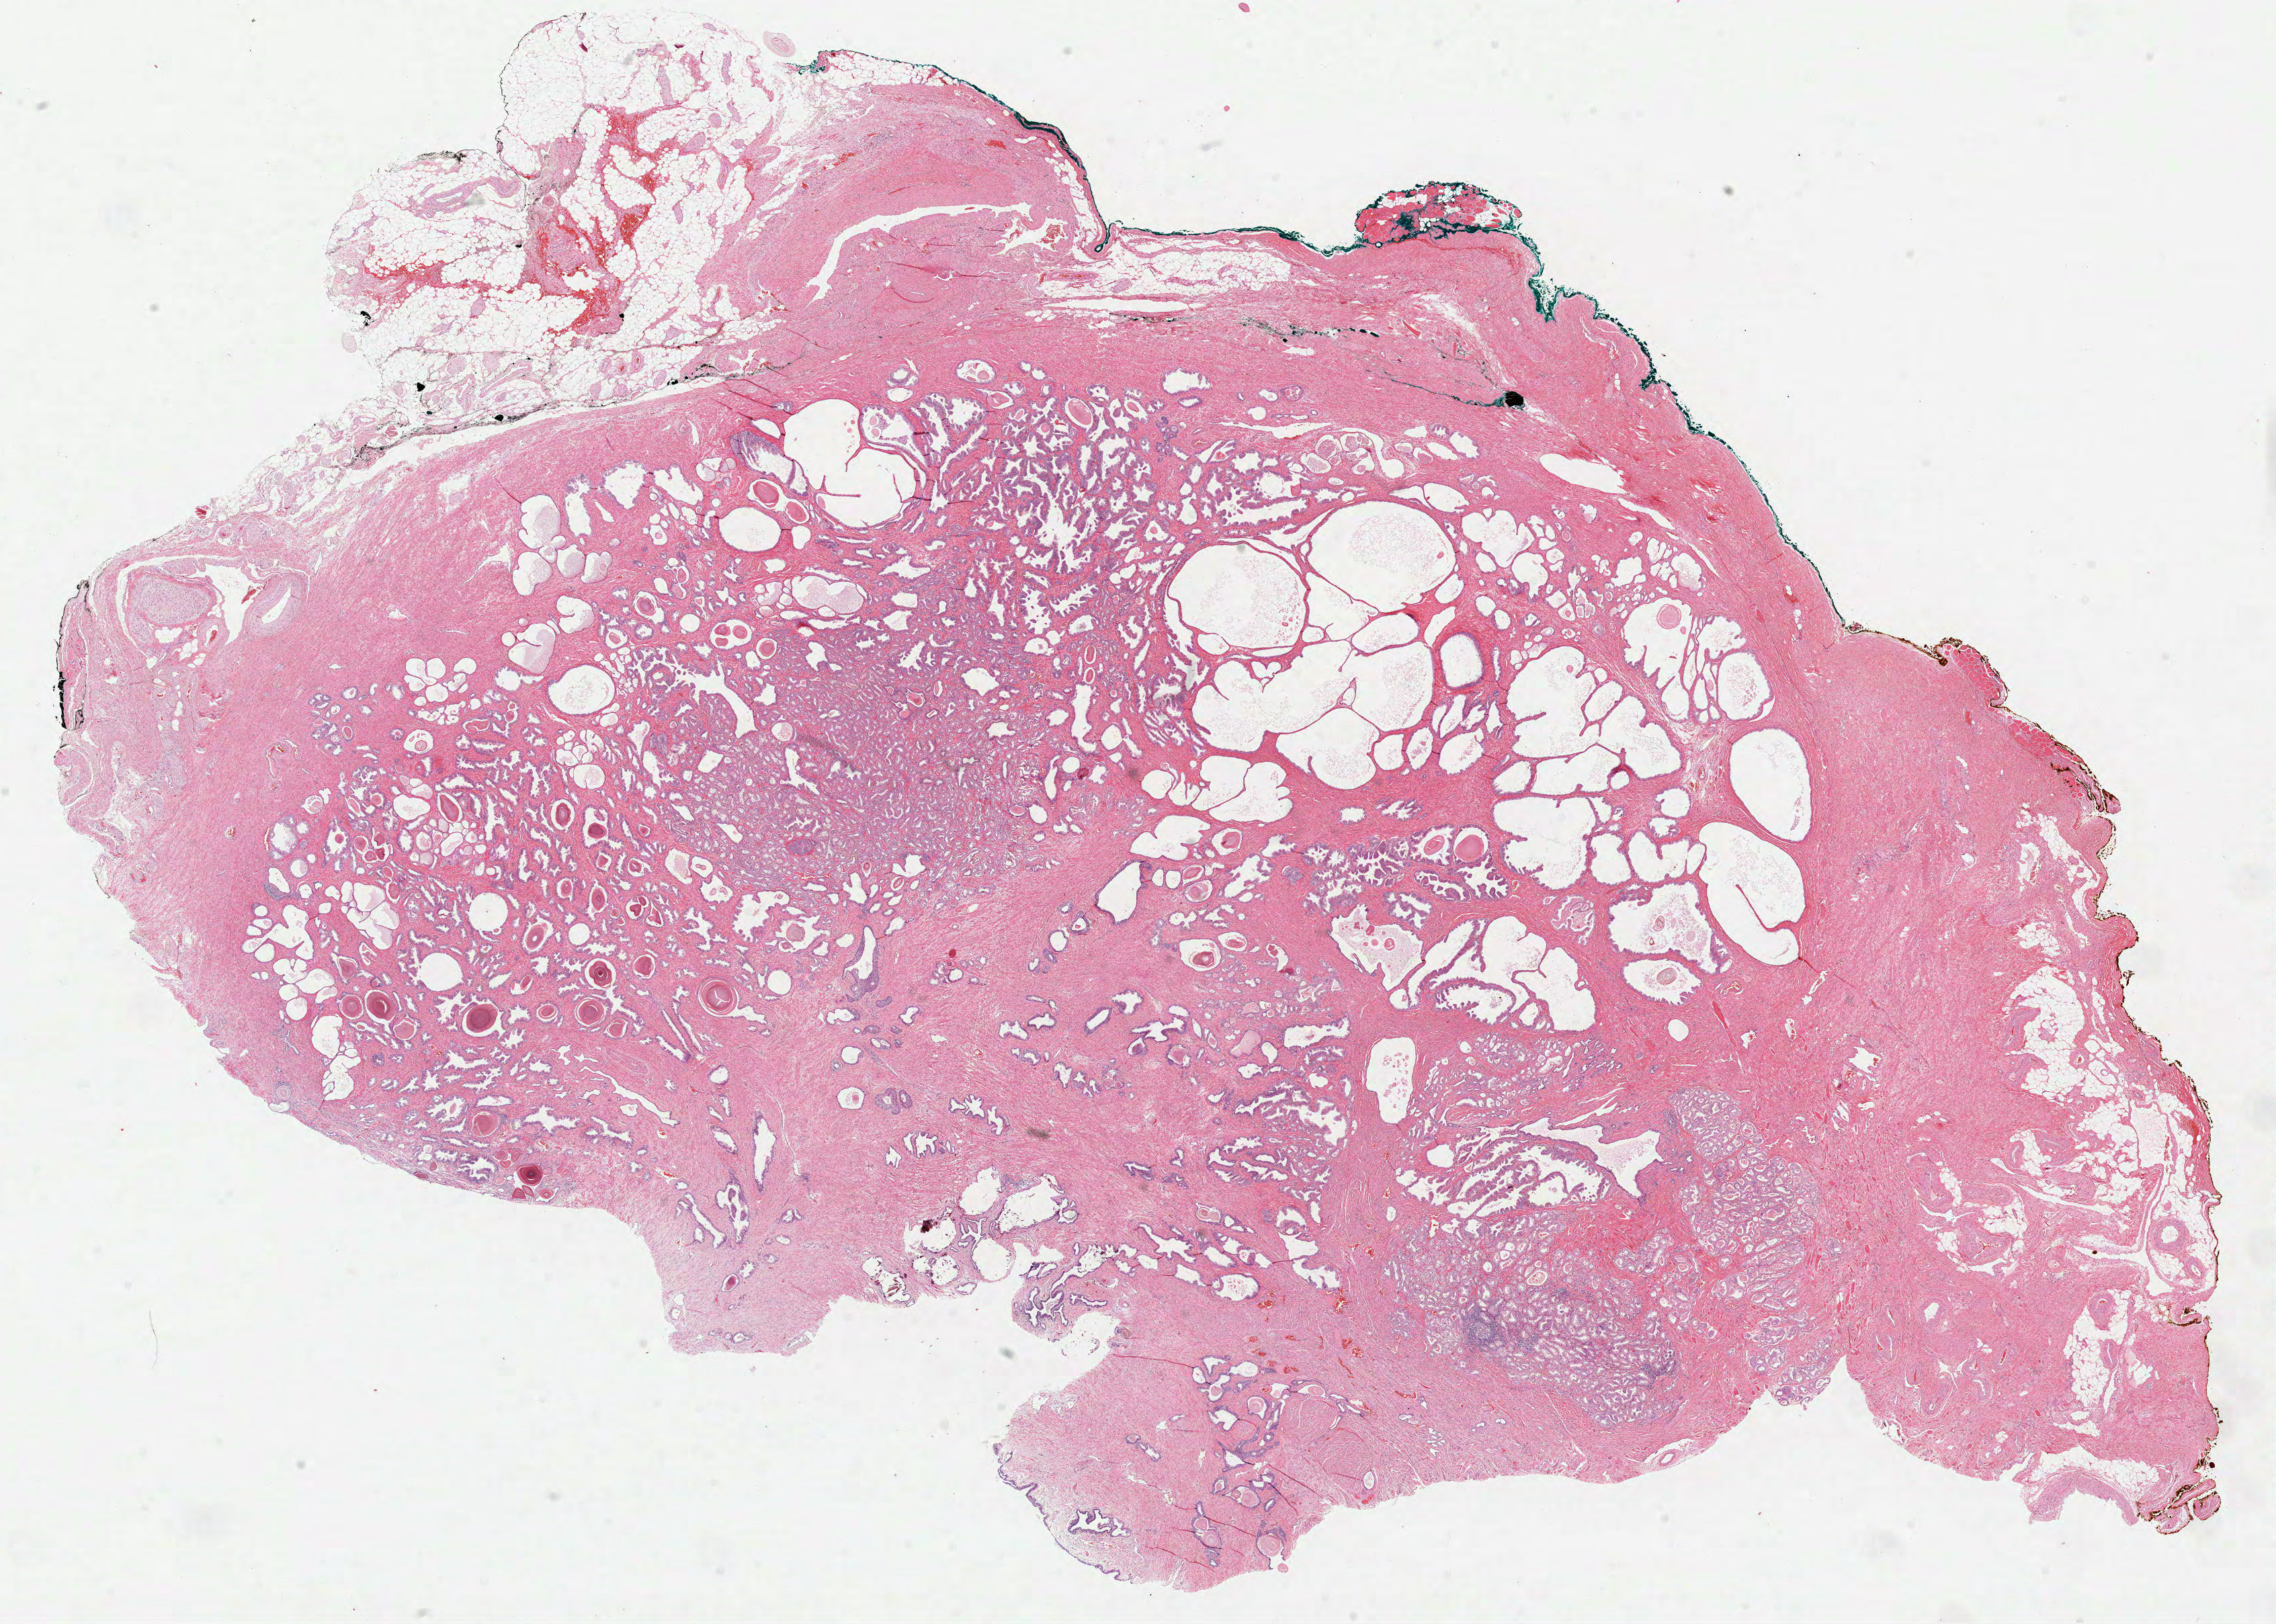
H&E whole-slide image, low-resolution overview of the scanned area, about 27.3 x 19.5 mm. FFPE section. Prostate, primary tumour sample. Male, age 61 years at initial diagnosis. Gleason score: 6 (3+3).
Pathologic diagnosis: Acinar cell carcinoma (prostate gland).